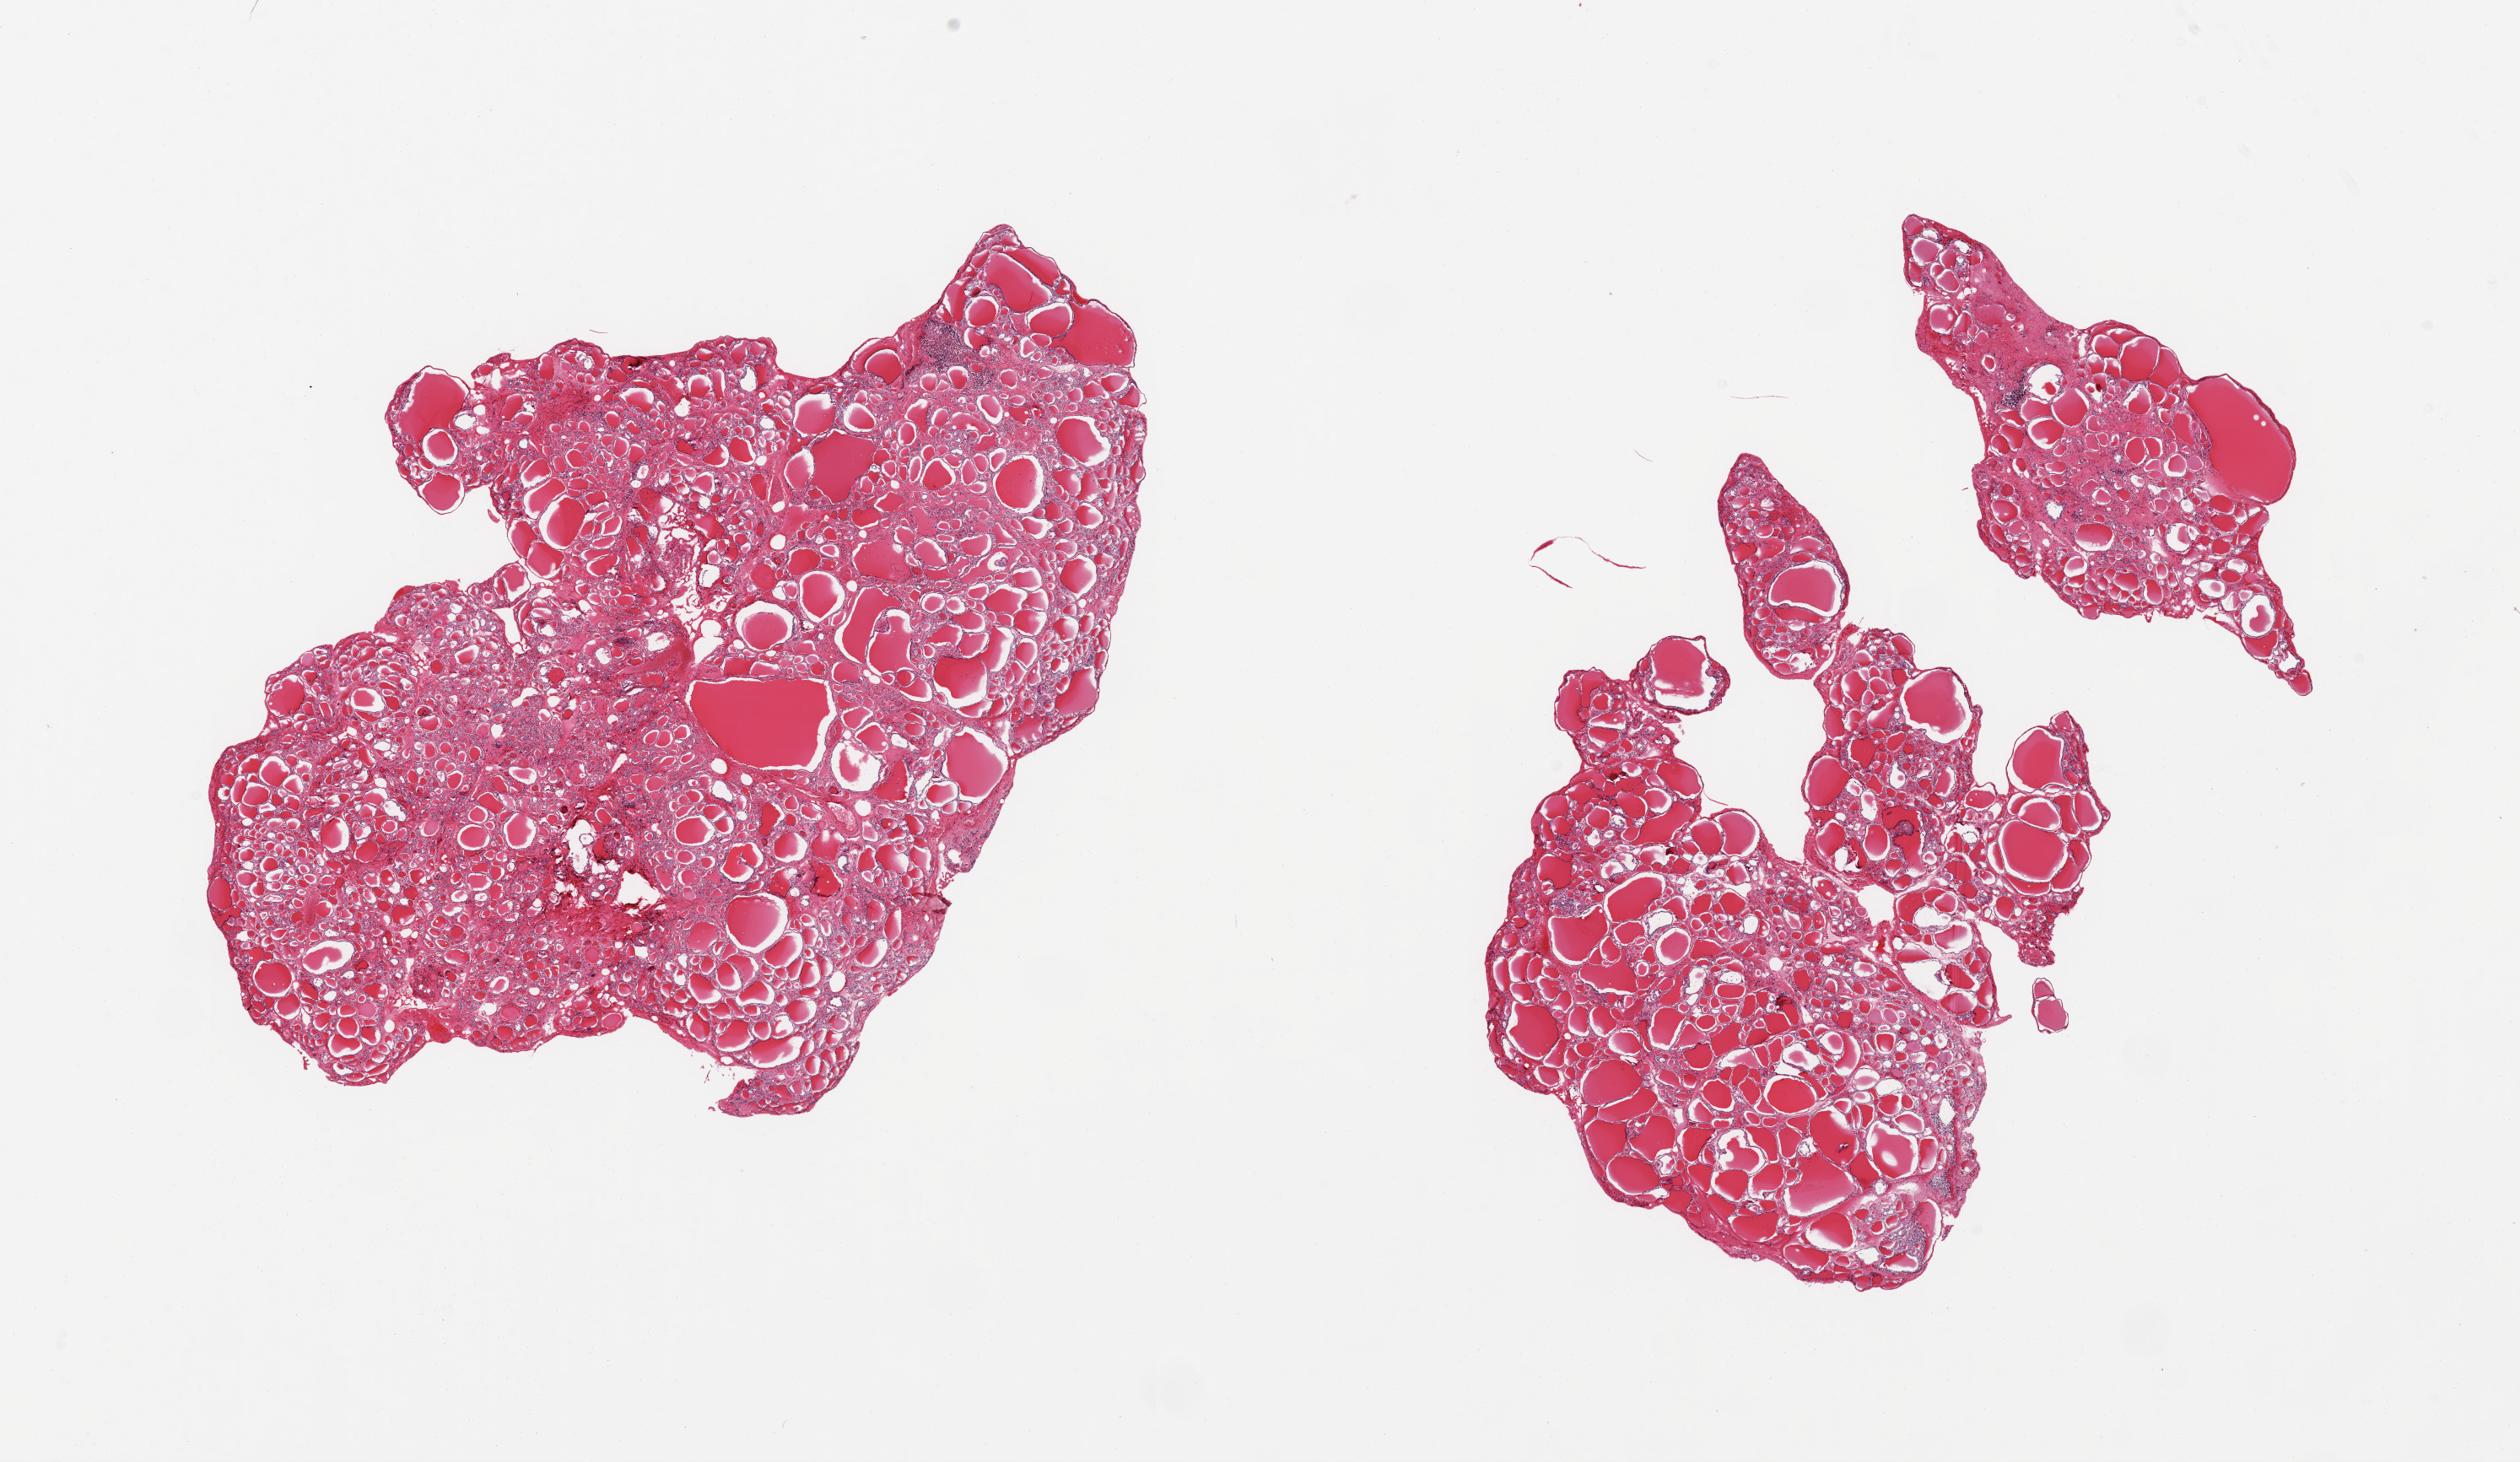
Whole-slide image, hematoxylin and eosin (H&E) stain — a low-resolution overview of the entire scanned area, about 23.6 x 13.7 mm, PAXgene-fixed paraffin-embedded (PFPE) section, target tissue: thyroid, tissue donor sample. Donor sex: male.
Review note (as recorded): 2 pieces; several small (<1mm) foci of lymphocytes.